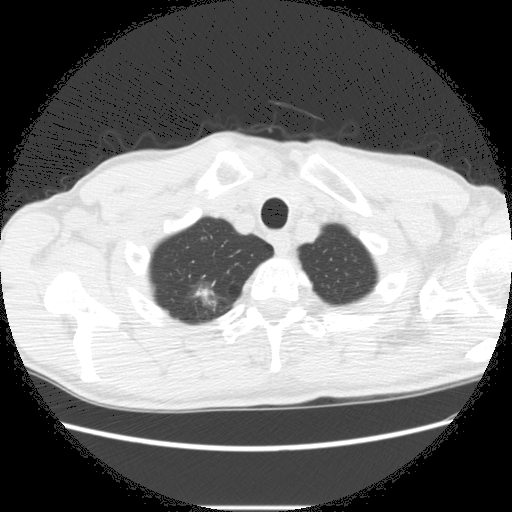
Low-dose screening chest CT, one axial slice; position 260 of 282 along the scan axis; reconstruction kernel STANDARD; lung window (W 1500 / L -600 HU); 2.5 mm slice thickness; 512 × 512 image matrix.
Outlined on this slice (outlined manually by an expert reader):
- lesion 2 (nodule, upper lobe of right lung): bounding box (x1, y1, x2, y2) in pixels: (192, 287, 216, 309)